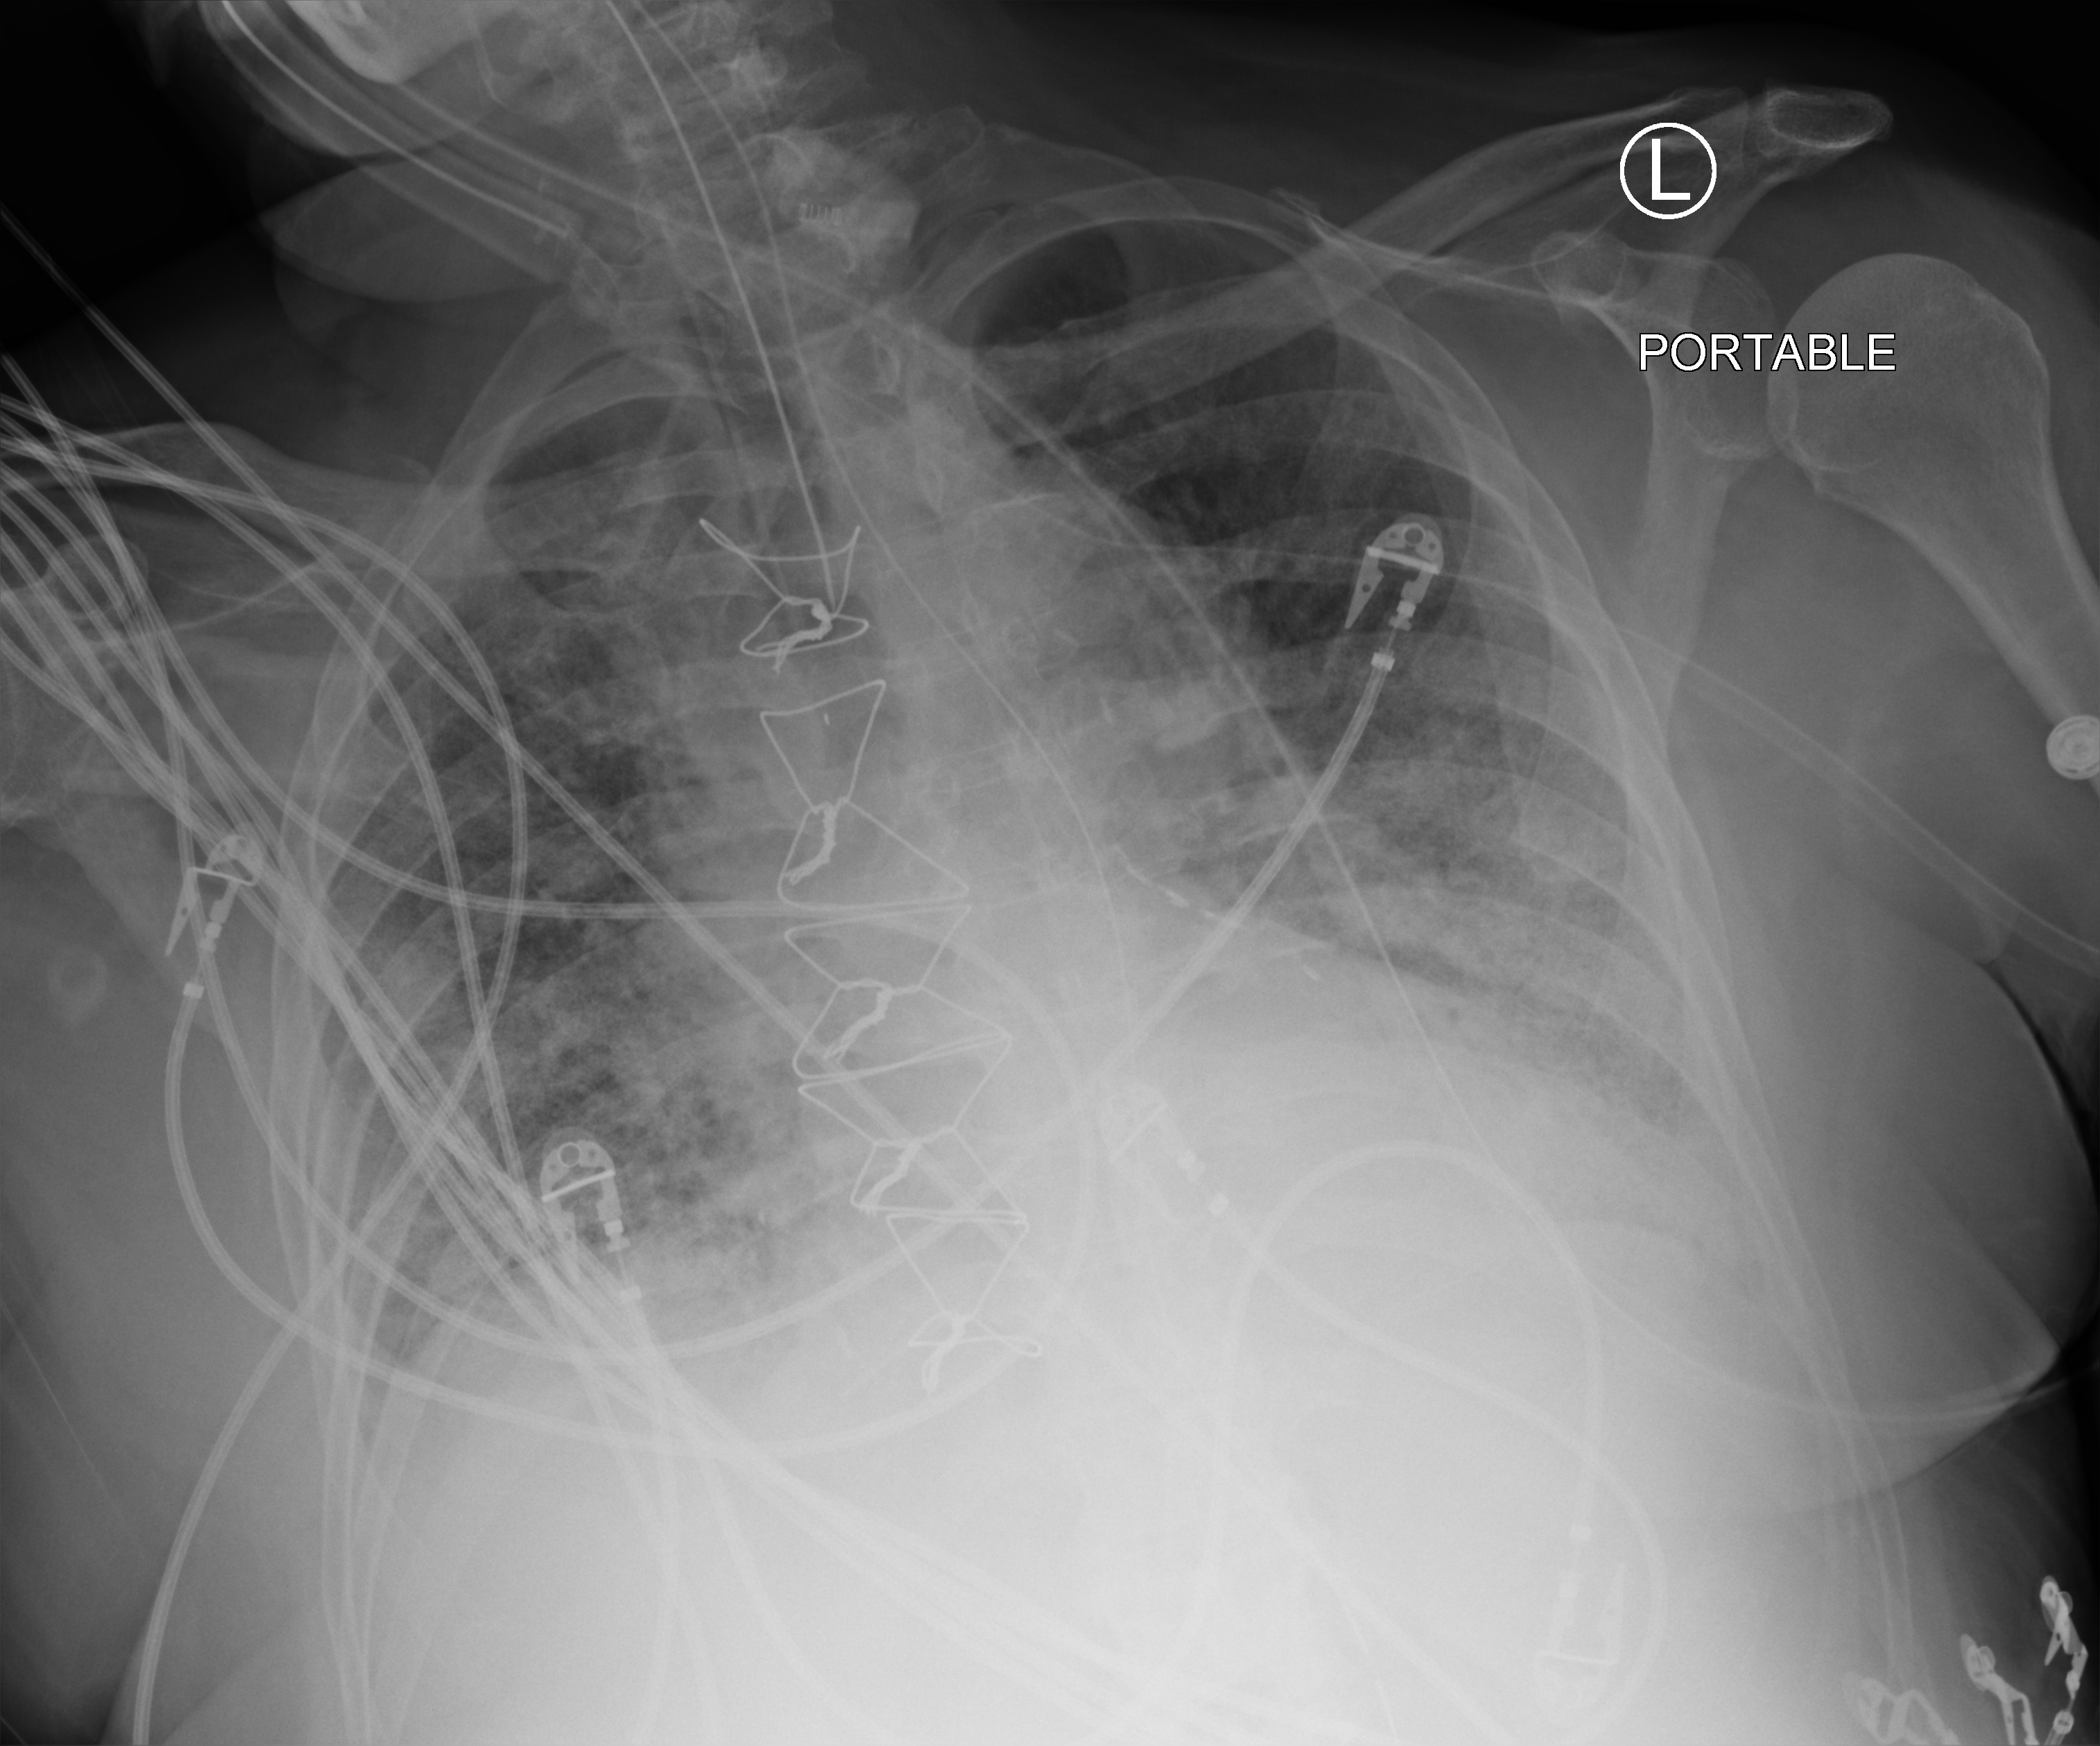
Chest X-ray (portable), anteroposterior (AP) projection. Male patient hospitalised with COVID-19, age 75–90 years.
Hospital-stay facts (about this admission, not read from this image; timing relative to this image not recorded): COPD (admission record): yes; mechanically ventilated during this hospital stay: yes.